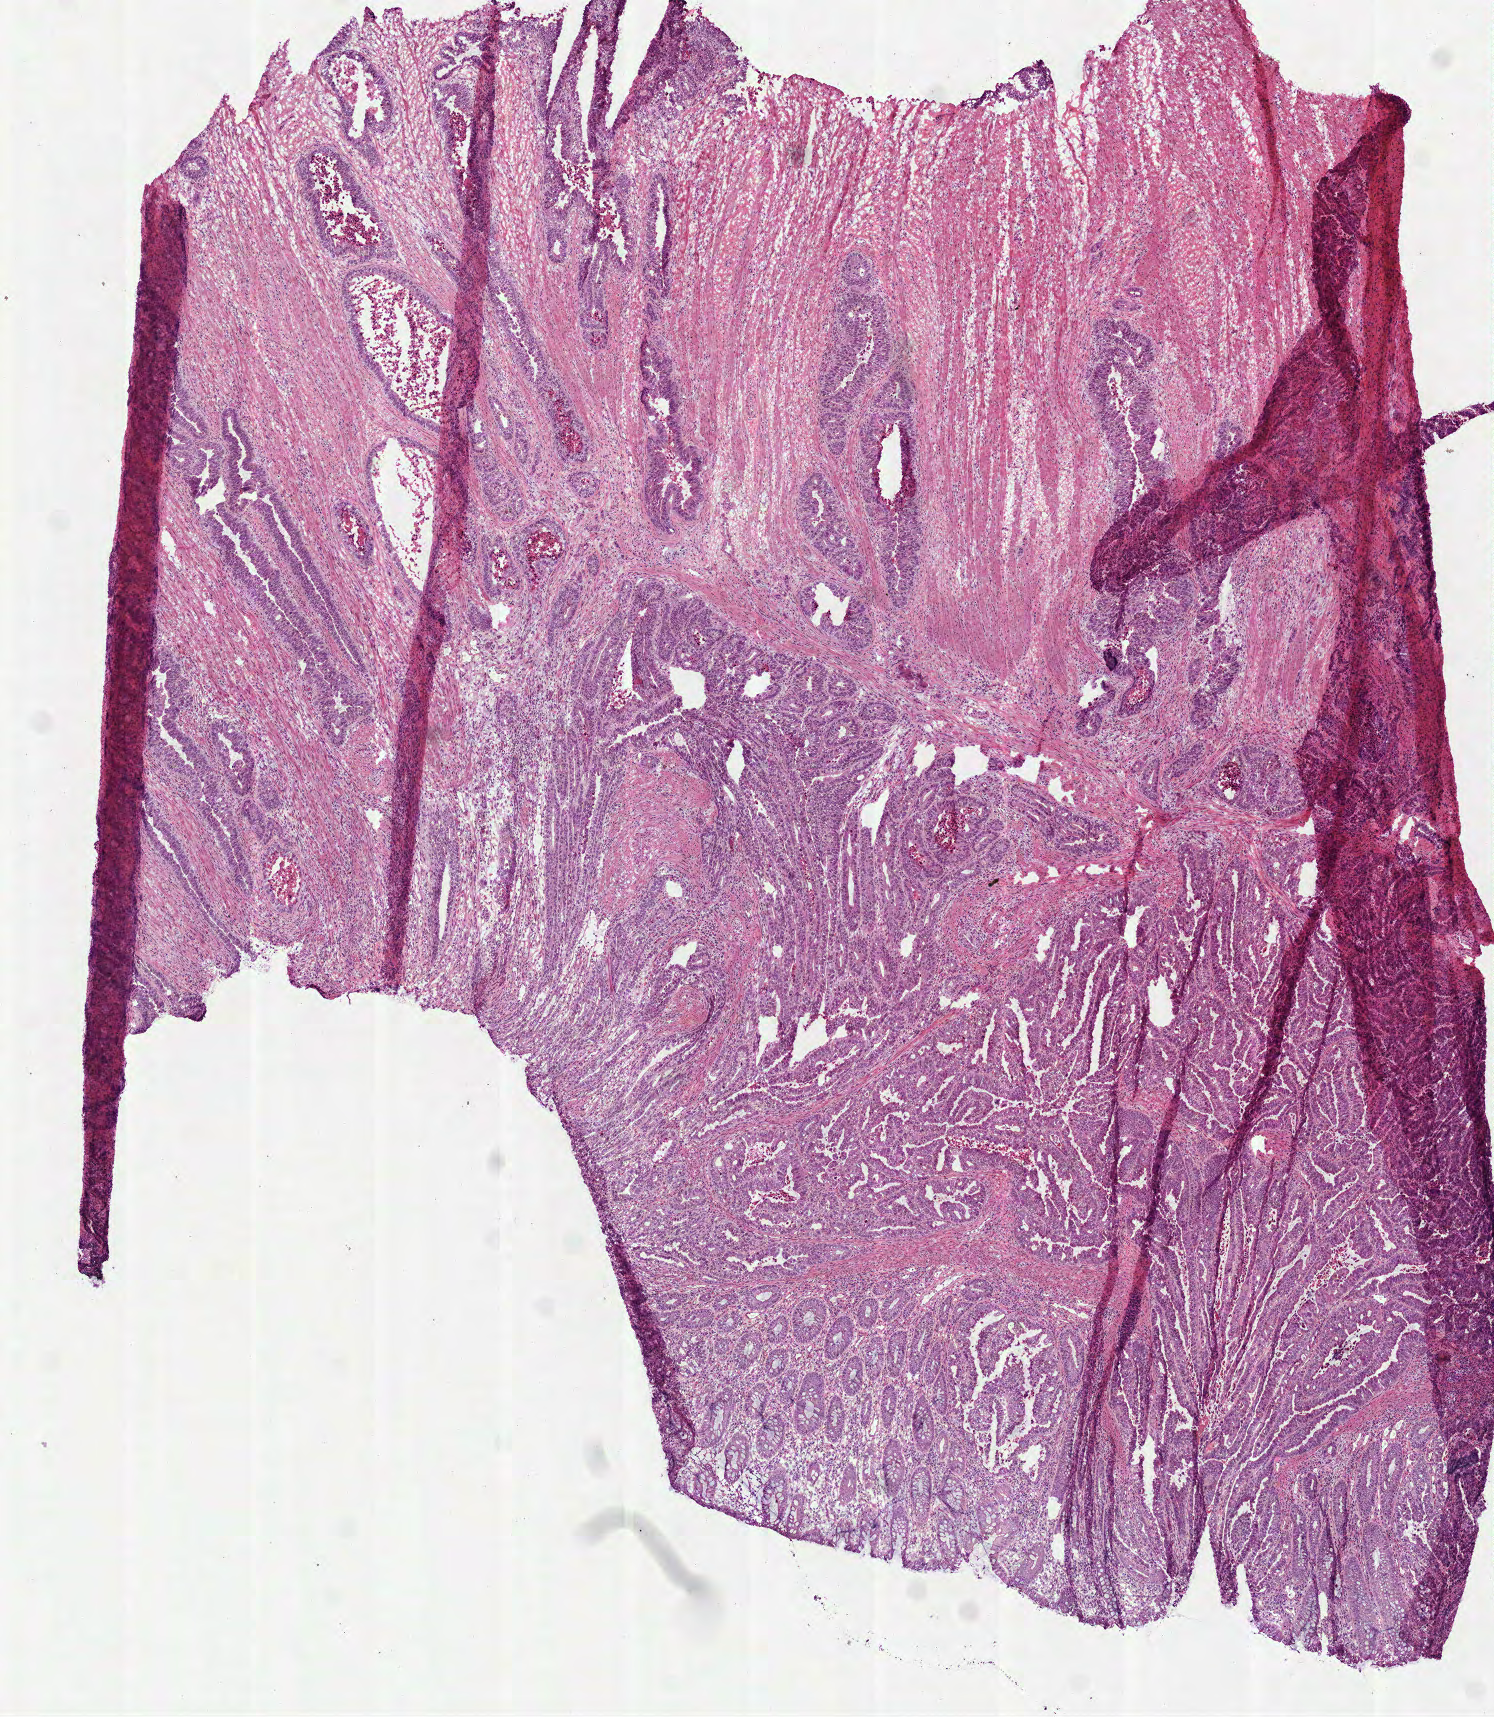
Digitized H&E tissue section (whole slide) — whole scanned area (about 6.0 x 6.9 mm, from a 40x scan) shown as a low-resolution overview. Frozen section from the top of the tissue portion. Sample: primary tumour, colon. Patient: male, age at initial diagnosis 66 years. Composition of this section per pathologist review: tumour cells 80%, tumour nuclei 71%, normal cells 10%, stromal cells 0%, necrosis 10%. Inflammatory infiltration, as recorded: lymphocyte infiltration 7%, monocyte infiltration 7%, neutrophil infiltration 7%.
Diagnosis: Adenocarcinoma, NOS (ascending colon). AJCC pathologic stage: IIIB.